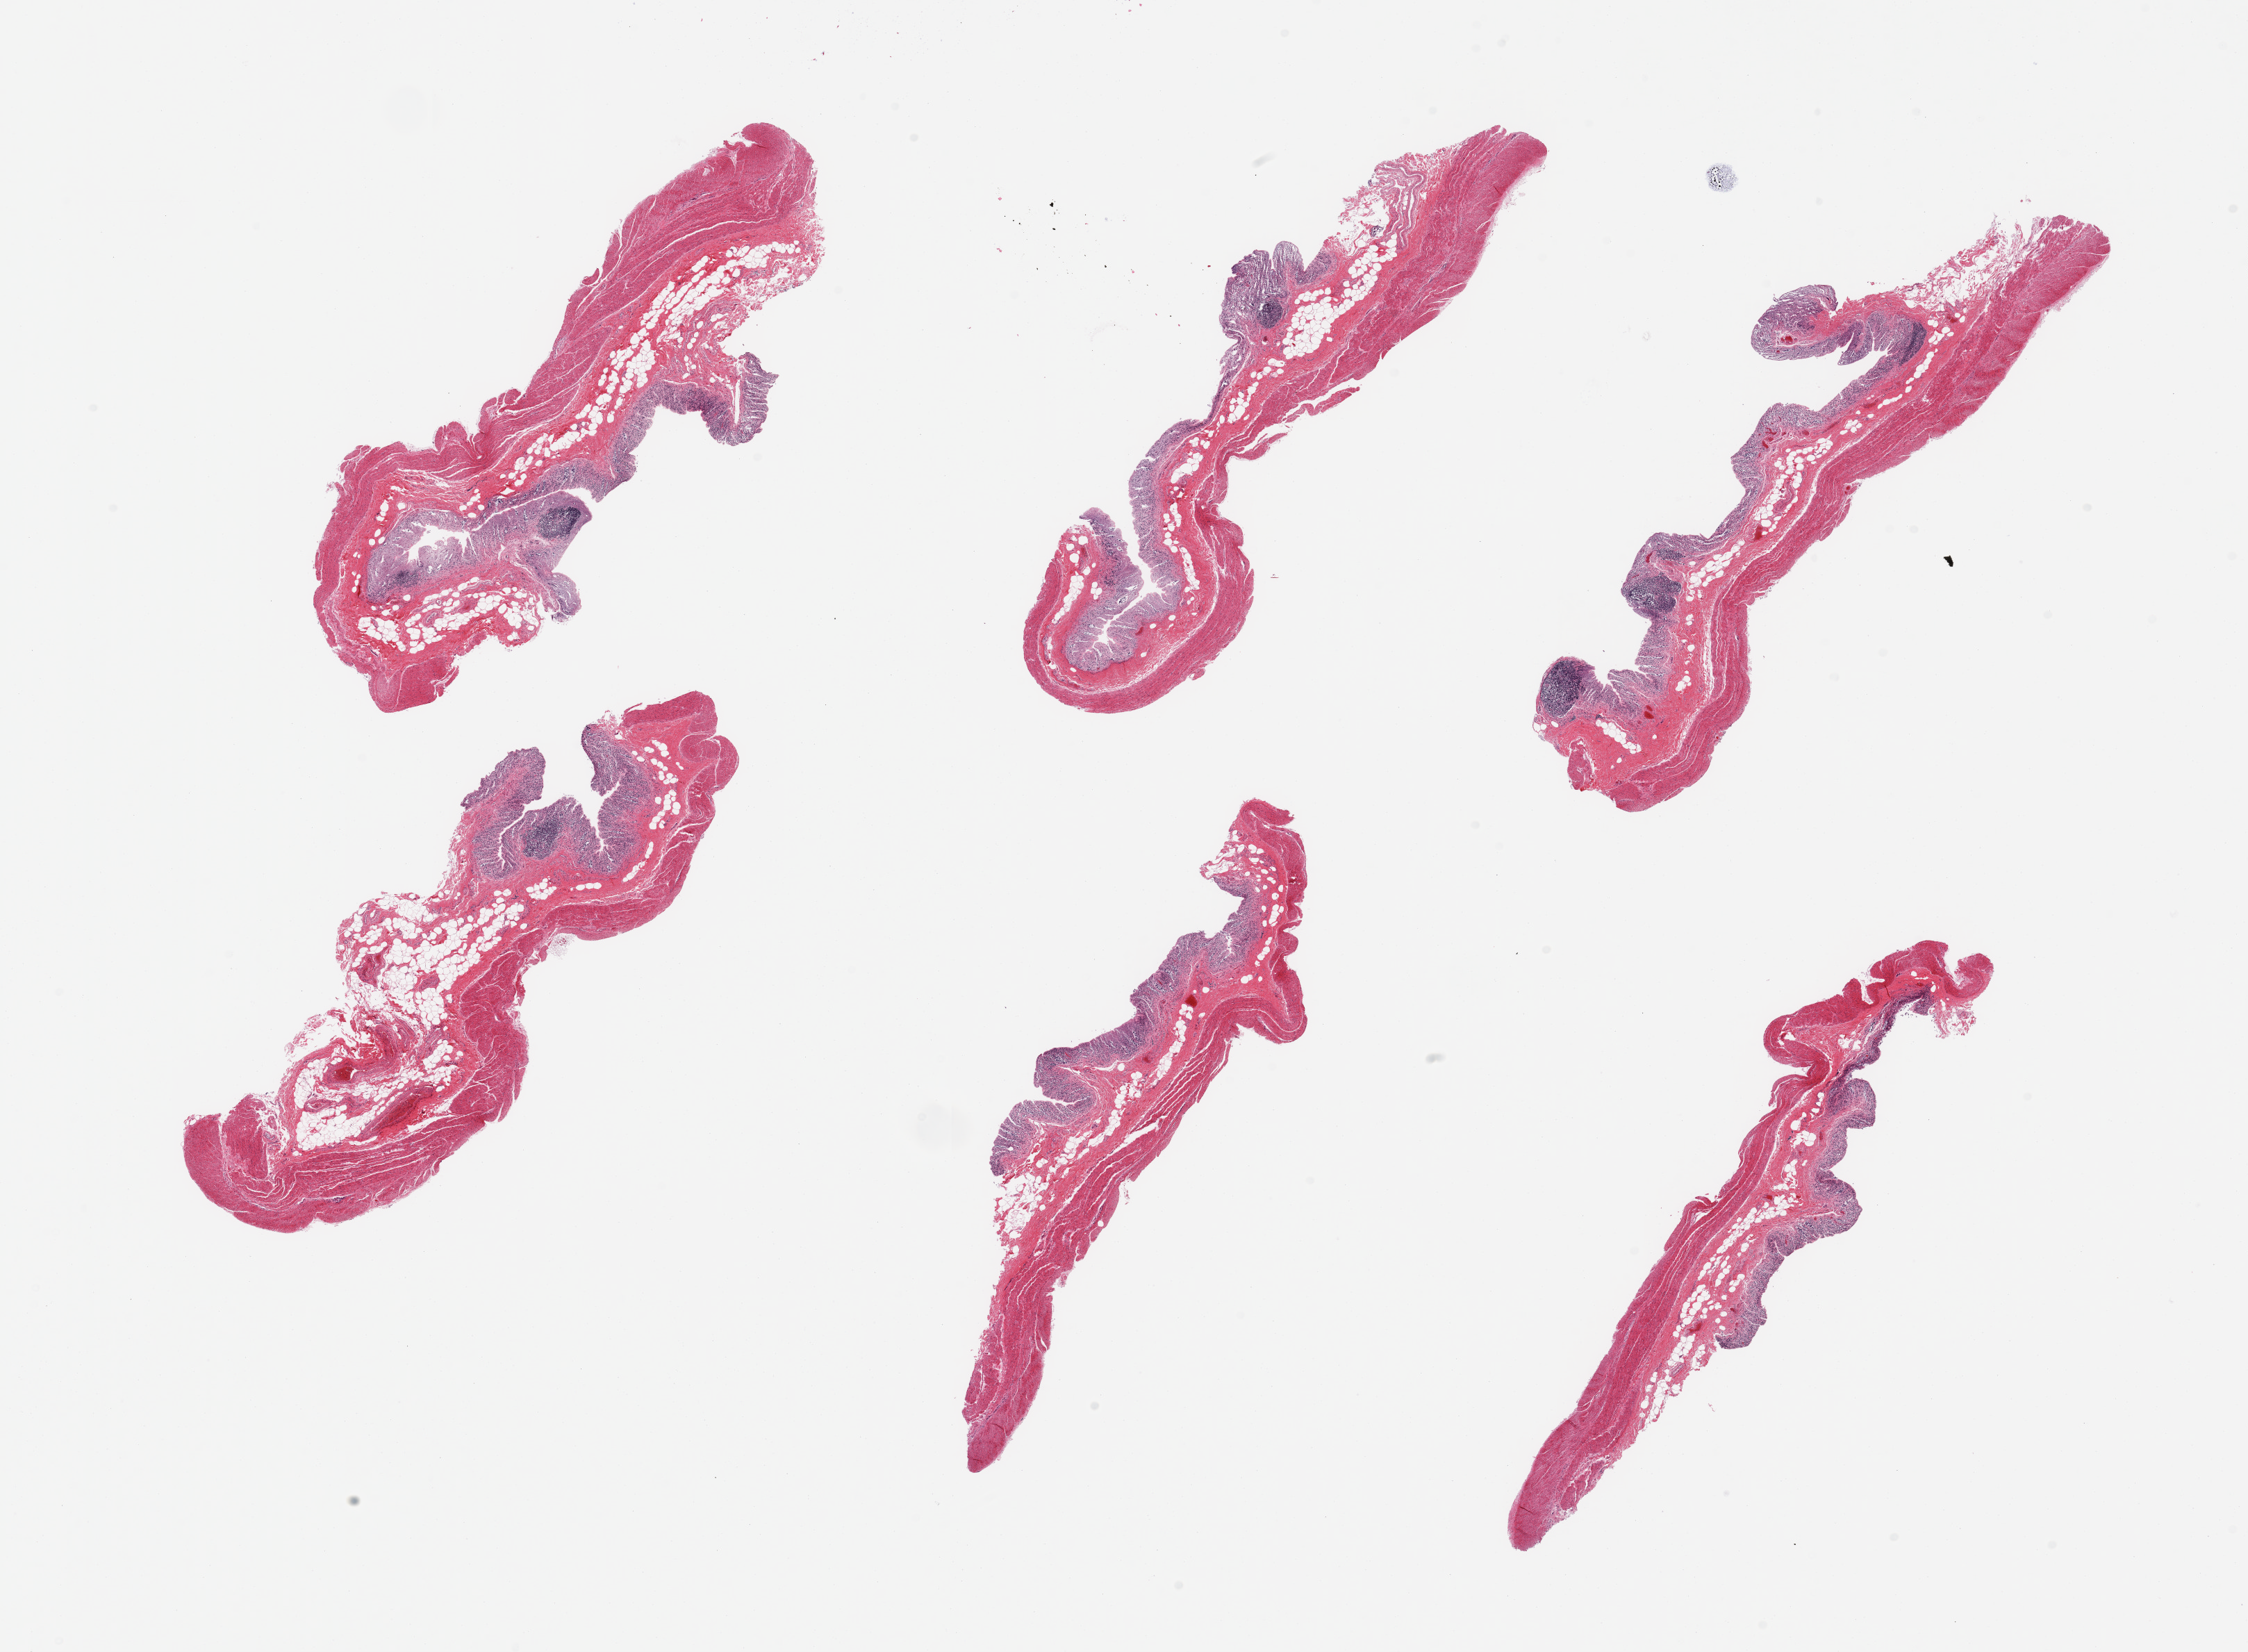
Digitized H&E-stained section, low-resolution overview of the scanned area, about 25.6 x 18.8 mm (acquisition: 20x scan), PAXgene-fixed paraffin-embedded (PFPE) section, target tissue: transverse colon, donor tissue sample. Donor: male.
* pathologist's review note for this sample: 6 pieces, target mucosa up to ~0.25mm, totally autolyzed